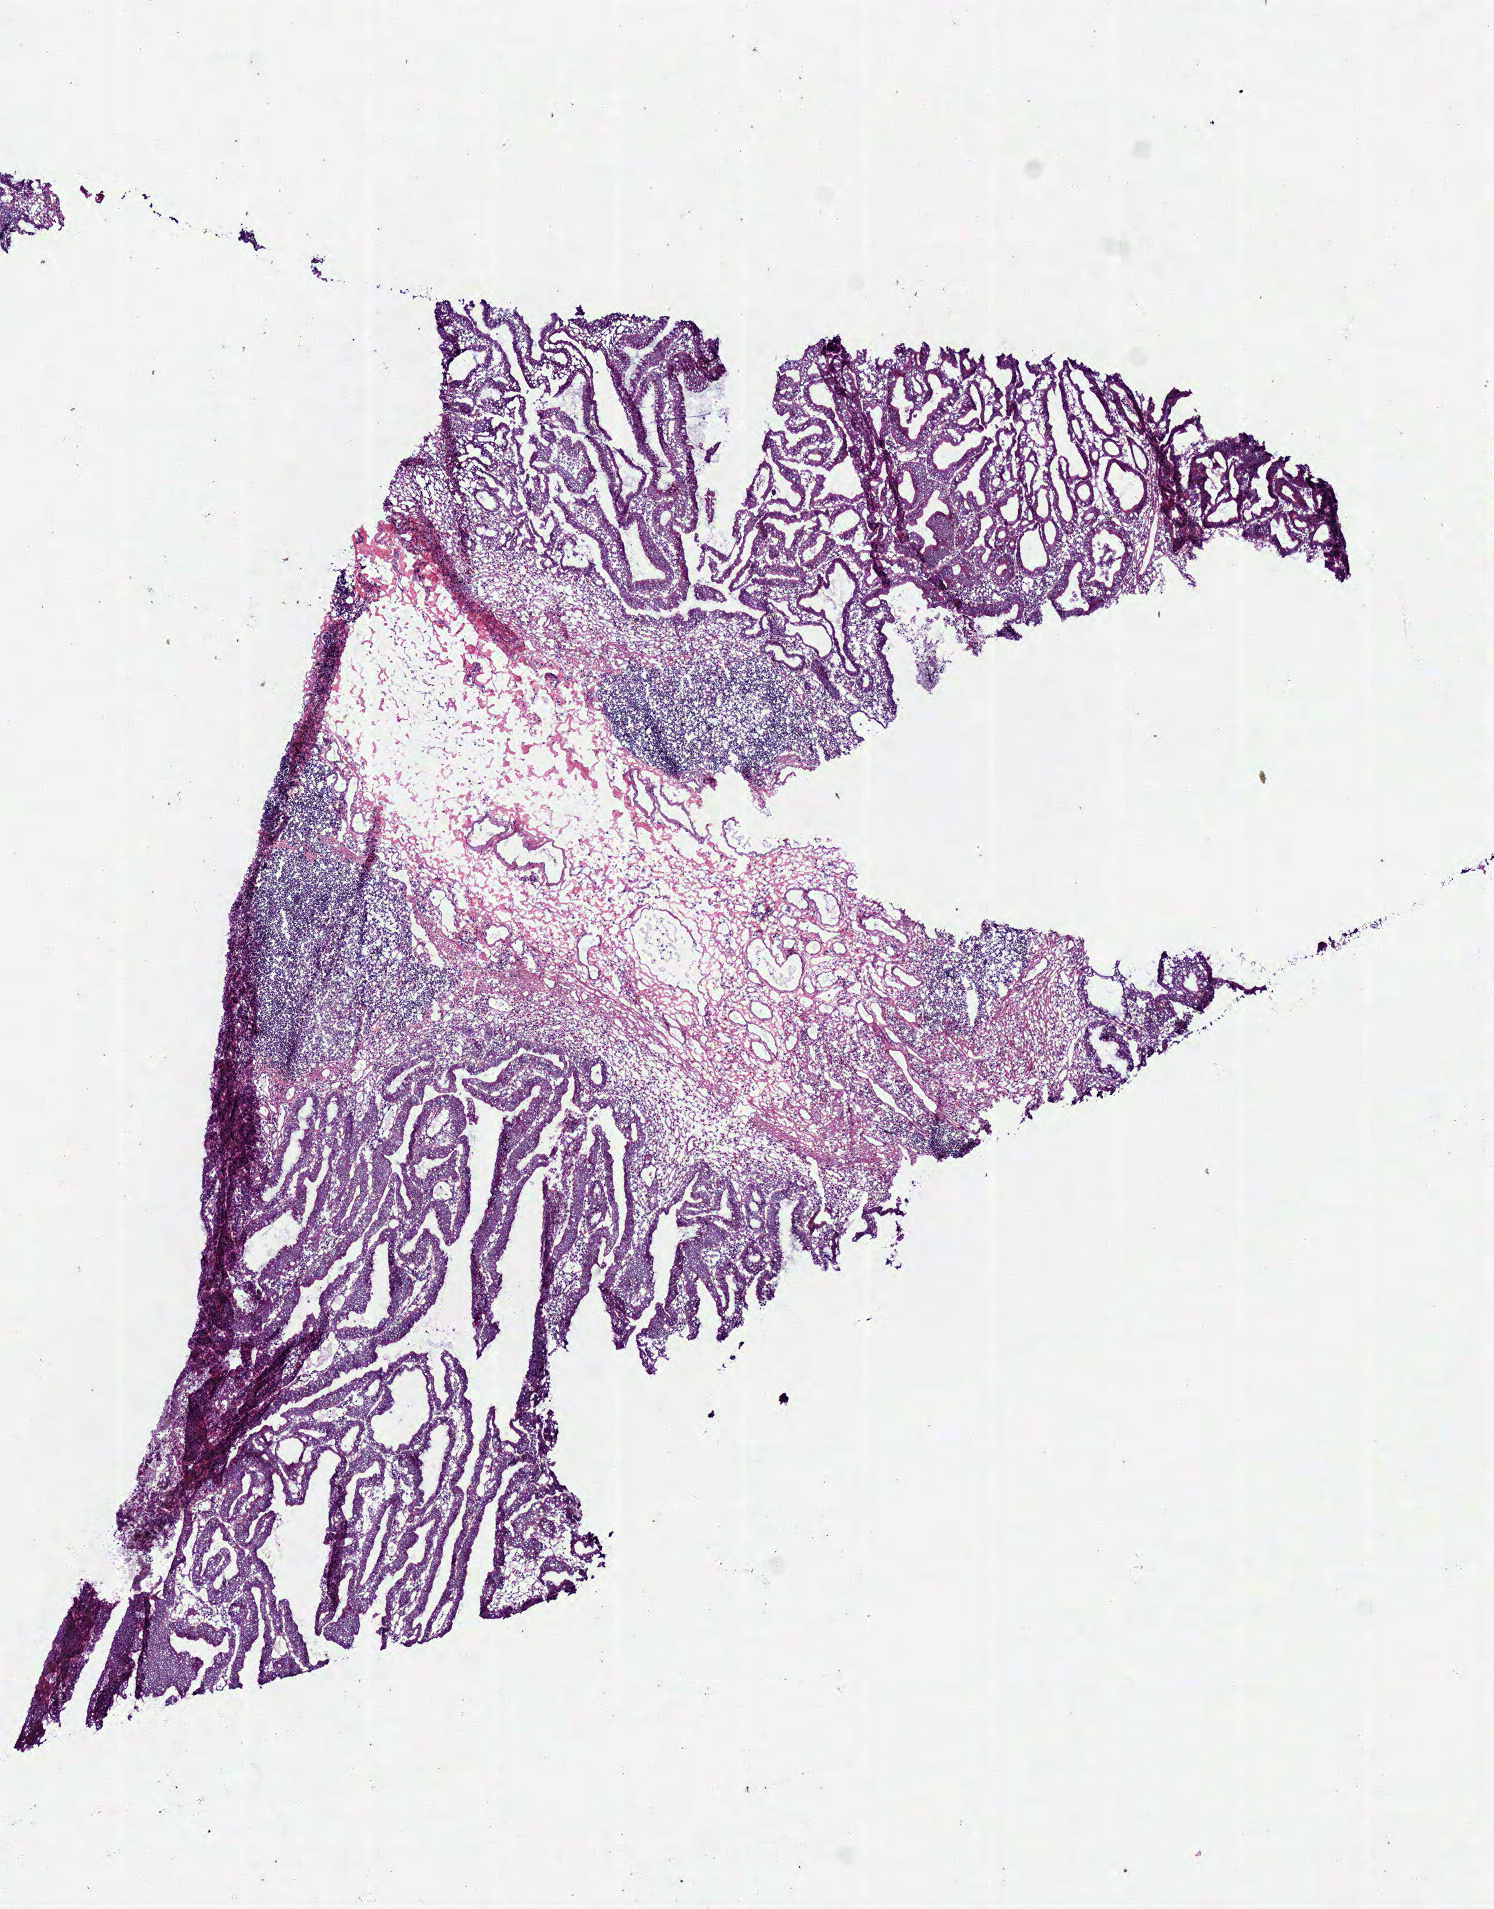
Digitized Hematoxylin and eosin (H&E) stained tissue section (whole slide), a low-resolution overview of the entire scanned area, about 5.9 x 7.5 mm (slide scanned at 40x); frozen section; sample: primary tumour, colon. Male patient; age at initial diagnosis 50 years. Composition of this section per pathologist review: tumour cells 70%, tumour nuclei 65%, normal cells 0%, stromal cells 30%, necrosis 0%.
AJCC pathologic stage: IA (7th edition). TNM: Tis N0 MX. Pathologic diagnosis: Adenocarcinoma, NOS (cecum).